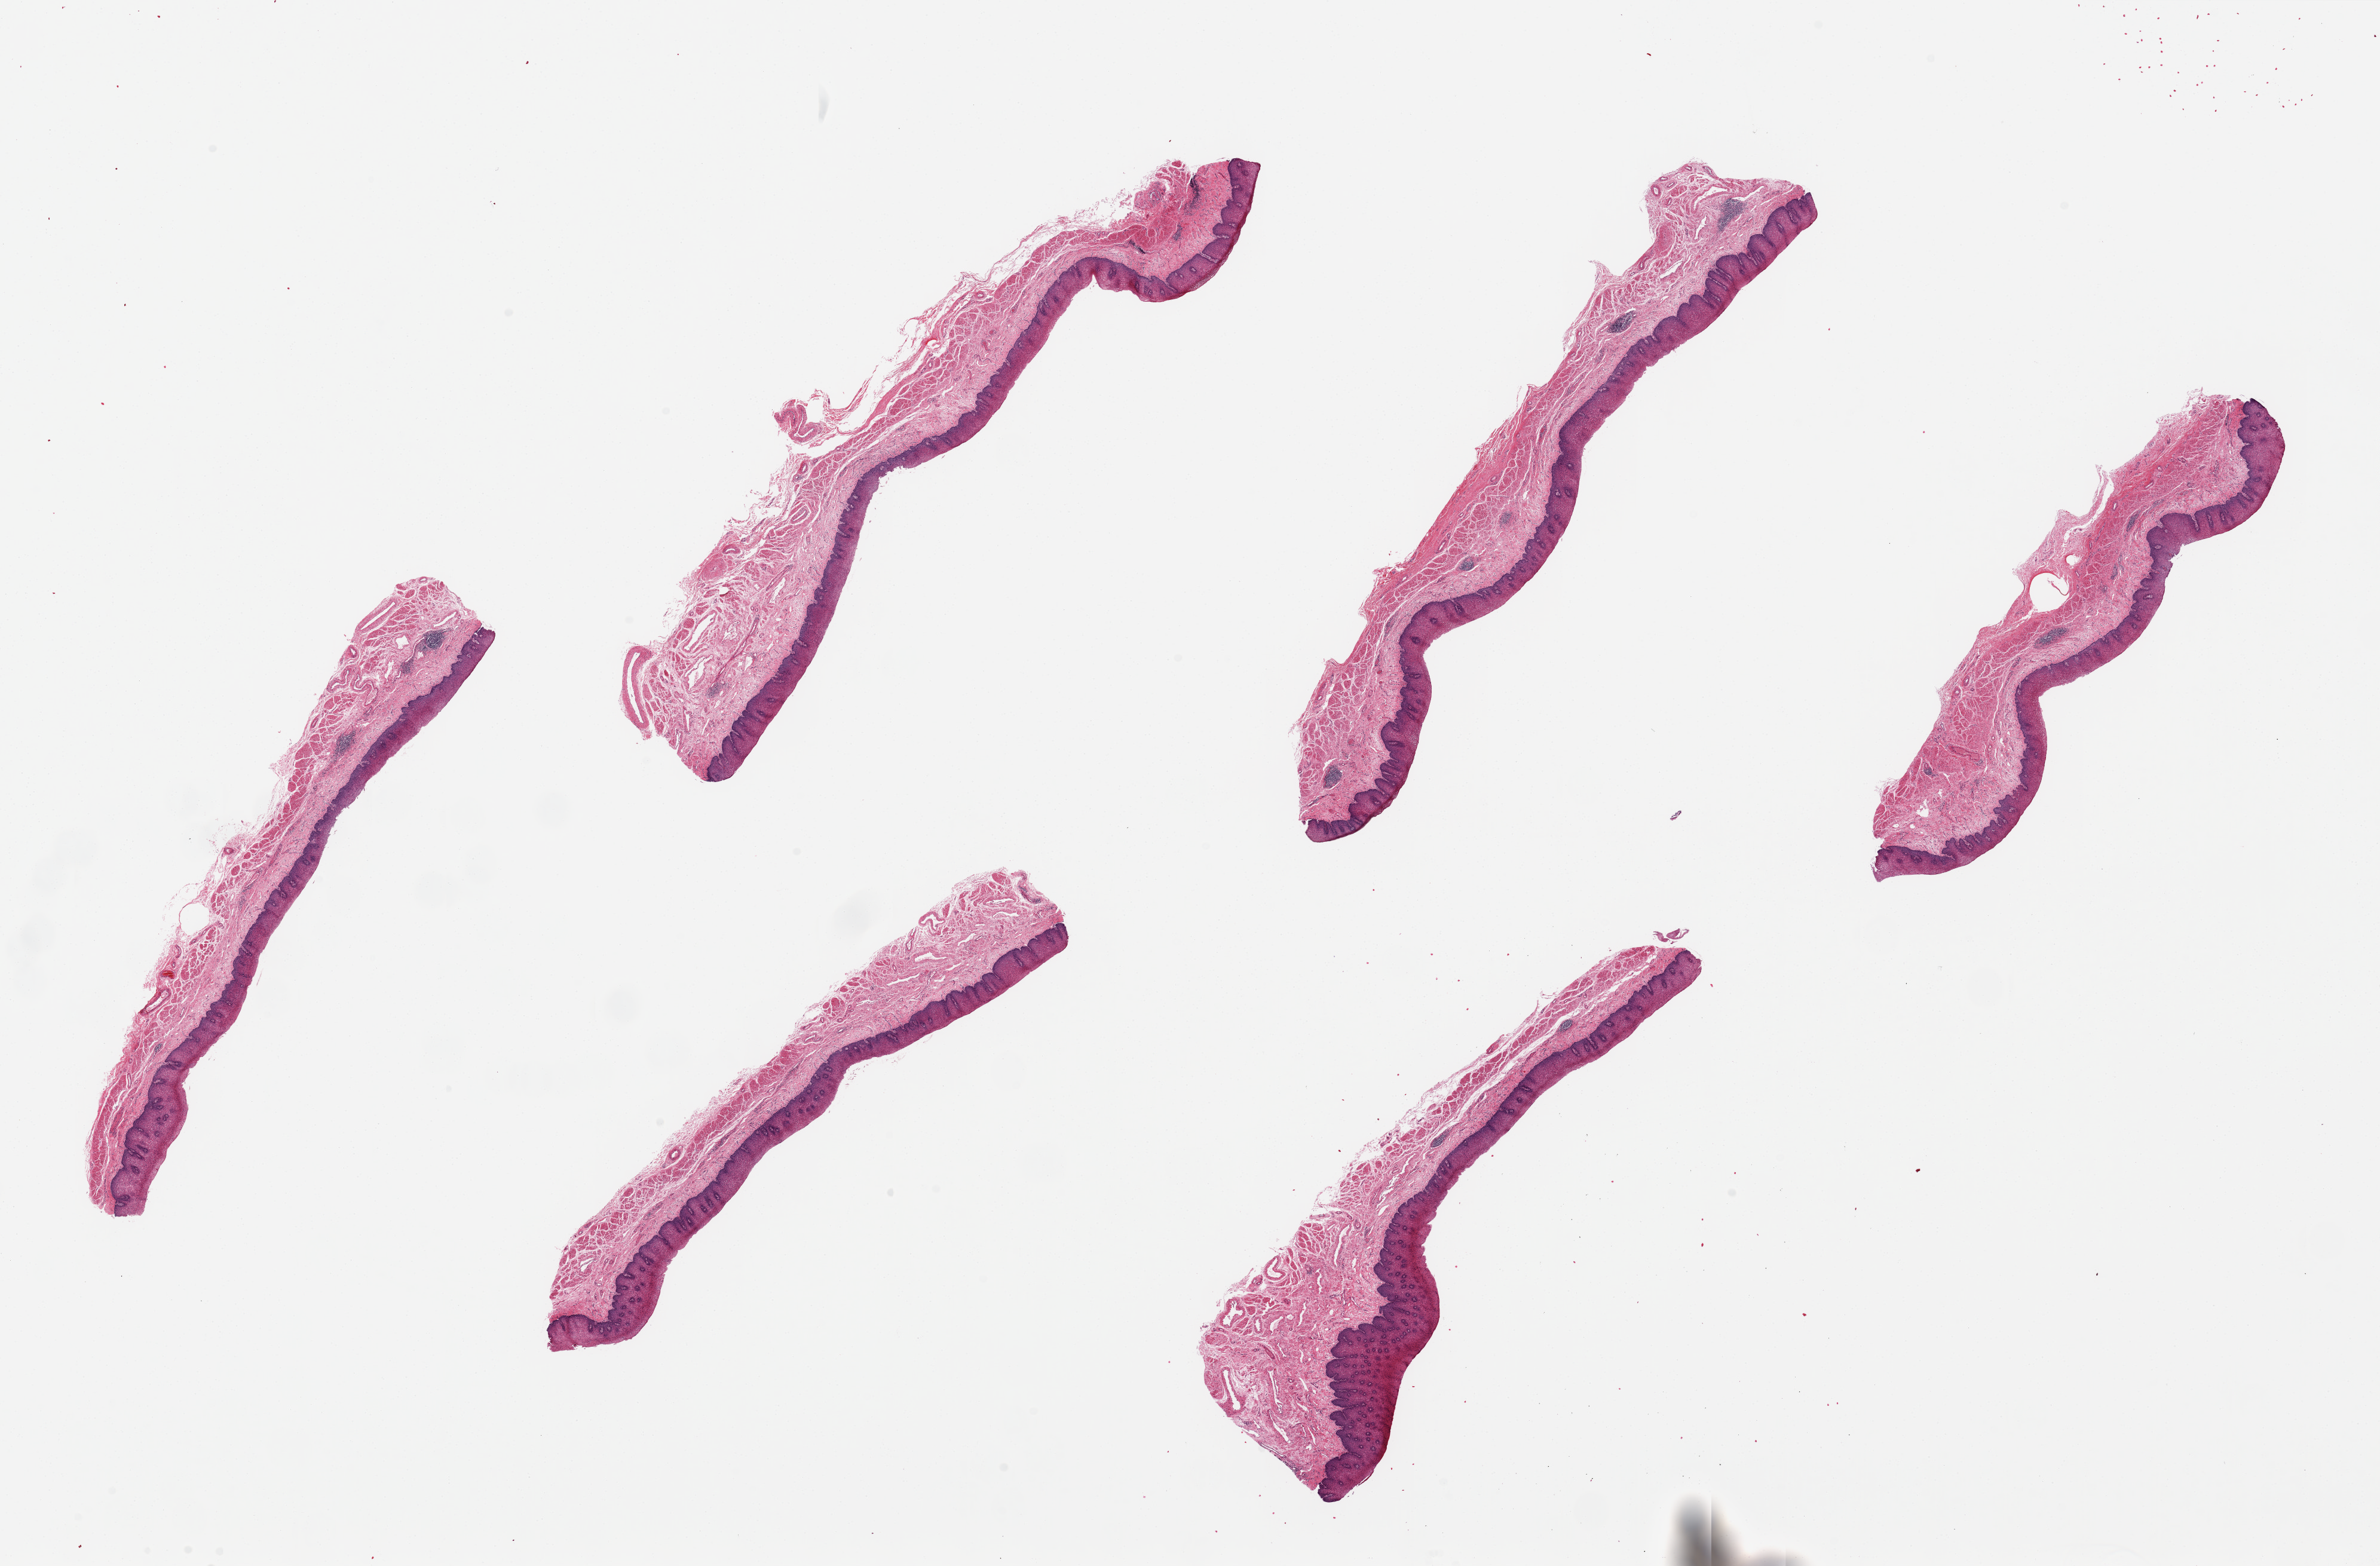
Whole-slide image, hematoxylin and eosin (H&E) stain, shown as a low-resolution overview of the whole scanned area (about 31.5 x 20.7 mm), PAXgene-fixed, paraffin-embedded tissue, sampled site (target tissue): esophageal mucous membrane, donor tissue sample. Donor: male.
Review note (as recorded): 6 pieces ~9x1.5mm. Squamous mucosa is ~10-15% of thickness.